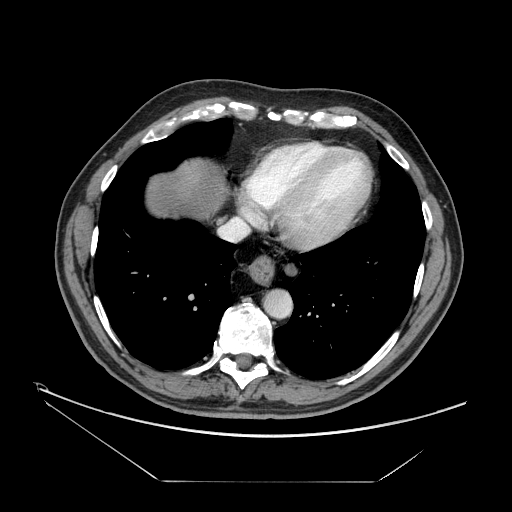
Contrast-enhanced abdominal CT, one axial slice. Position 152 of 161 along the scan axis. Reconstruction kernel STANDARD. 120 kVp. Intravenous contrast given. Soft-tissue window (W 400 / L 40 HU). 2.5 mm slice thickness. 512 × 512 image matrix, field of view 440 × 440 mm. Male patient, age 65 years. From the clinical record (not read from this slice): diagnosis: colorectal cancer liver metastases, imaged before liver resection; multiple liver metastases: yes; largest metastasis: 4.2 cm; disease in both lobes: yes.
Outlined on this slice (manually delineated by an expert):
- hepatic veins: bounding box <219,162,267,241> (left, top, right, bottom; pixels)
- liver: <144,158,225,217>
- planned liver remnant (the part of the liver to remain after resection): <145,158,226,218>